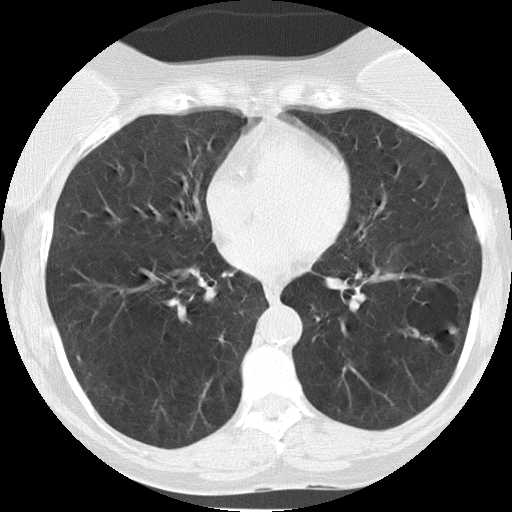
Chest CT (low-dose screening protocol), one axial image, first (baseline) screen, lung window (W 1500 / L -600 HU), 2 mm slice thickness, slice 83 of 149 in the series. Female participant, aged 58 years at enrolment. Current smoker at enrolment.
- Lesion marked by an expert reader, bounding box <400,314,459,354> (left, top, right, bottom; pixels).
- The screening reader recorded 3 non-calcified nodules or masses ≥4 mm on this exam (right lower lobe, lingula, left lower lobe); which of them this box marks is not recorded.